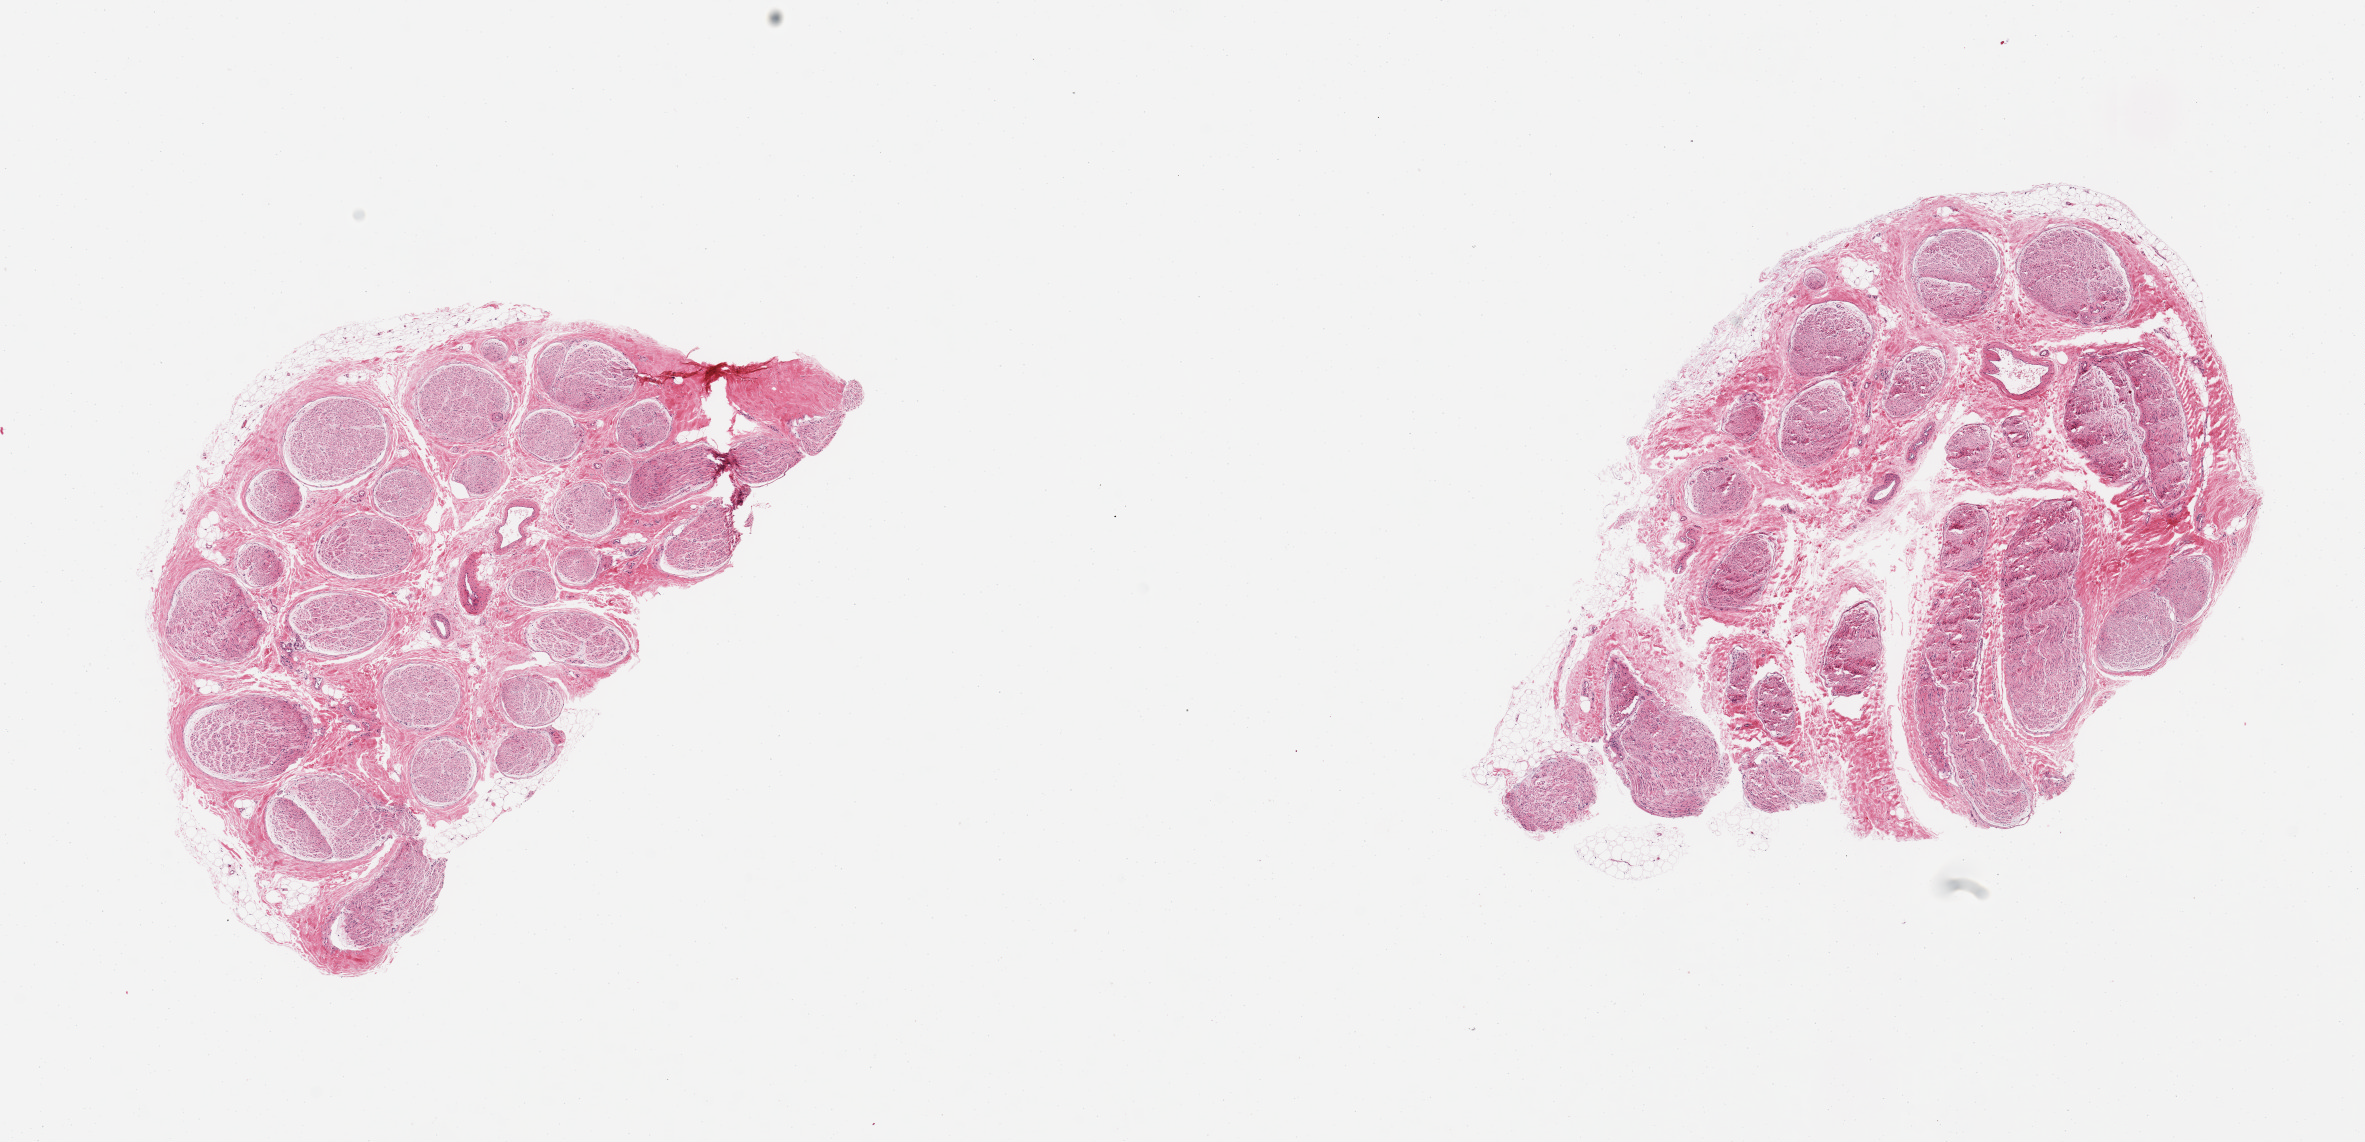
Digitized hematoxylin and eosin (H&E)-stained section, a low-resolution overview of the entire scanned area, about 18.7 x 9.0 mm, PAXgene-fixed, paraffin-embedded tissue, sampled site (target tissue): tibial nerve, donor tissue sample. Male donor.
Pathologist's review note for this sample: 2 pieces; nerve with trivial attachment of fat.